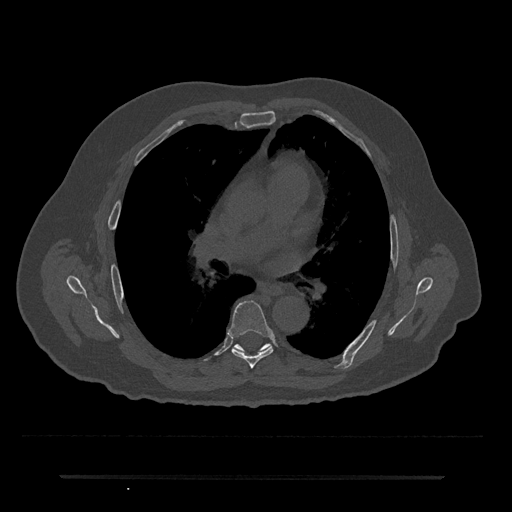
CT including the spine, one axial slice; position 424 of 797 along the scan axis; reconstruction kernel Br40s/3; 120 kVp; bone window (W 1800 / L 400 HU); 512 × 512 image matrix, field of view 437 × 437 mm. Patient: male, 69 years. Case-level facts recorded for this patient, not image findings: primary cancer: prostate.
Annotated regions visible in this slice (semi-automatic segmentation, software-assisted and operator-edited):
- T6 vertebra: bounding box [x1, y1, x2, y2] px = [229, 301, 273, 368]
- T7 vertebra: [234, 345, 242, 350]